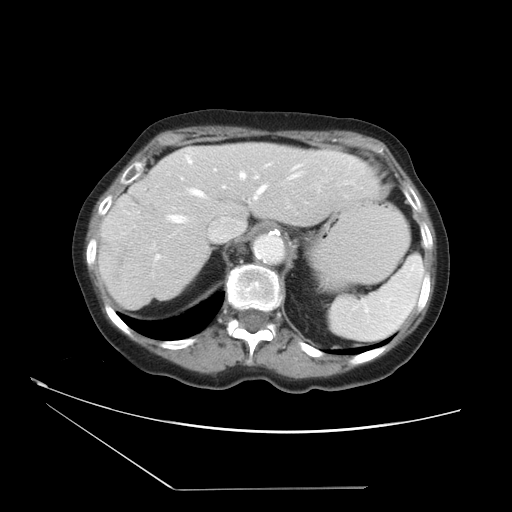
Contrast-enhanced abdominal CT, one axial slice; slice 26 of 36 in the series (ordered by position); 120 kVp; intravenous contrast given; soft-tissue window (W 400 / L 40 HU); 5 mm slice thickness; 512 × 512 image matrix, field of view 384 × 384 mm. Female patient, age 81 years. Case-level facts recorded for this patient, not image findings: diagnosis: colorectal cancer liver metastases, imaged before liver resection; multiple liver metastases: no; largest metastasis: 1.6 cm; disease in both lobes: no.
Outlined on this slice (manually delineated by an expert):
- hepatic veins: bounding box [x1, y1, x2, y2] px = [166, 158, 303, 224]
- liver: [99, 143, 381, 310]
- planned liver remnant (the part of the liver to remain after resection): [99, 143, 382, 310]
- portal vein (with intrahepatic branches): [156, 177, 257, 258]